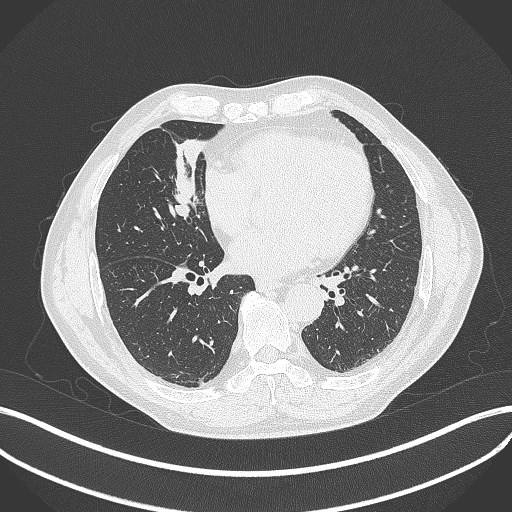
Chest CT, one axial slice. Slice 163 of 429 in the series (ordered by position). 120 kVp. Lung window (W 1500 / L -600 HU). 512 × 512 image matrix. Patient: male, 61 years. From the clinical record (not read from this slice): clinical TNM (as recorded): T2b N1 M0.
Structures marked on this image (bounding box drawn by a radiologist):
- lung tumour (recorded histology: squamous cell carcinoma): bounding box [x1, y1, x2, y2] px = [164, 165, 203, 220]